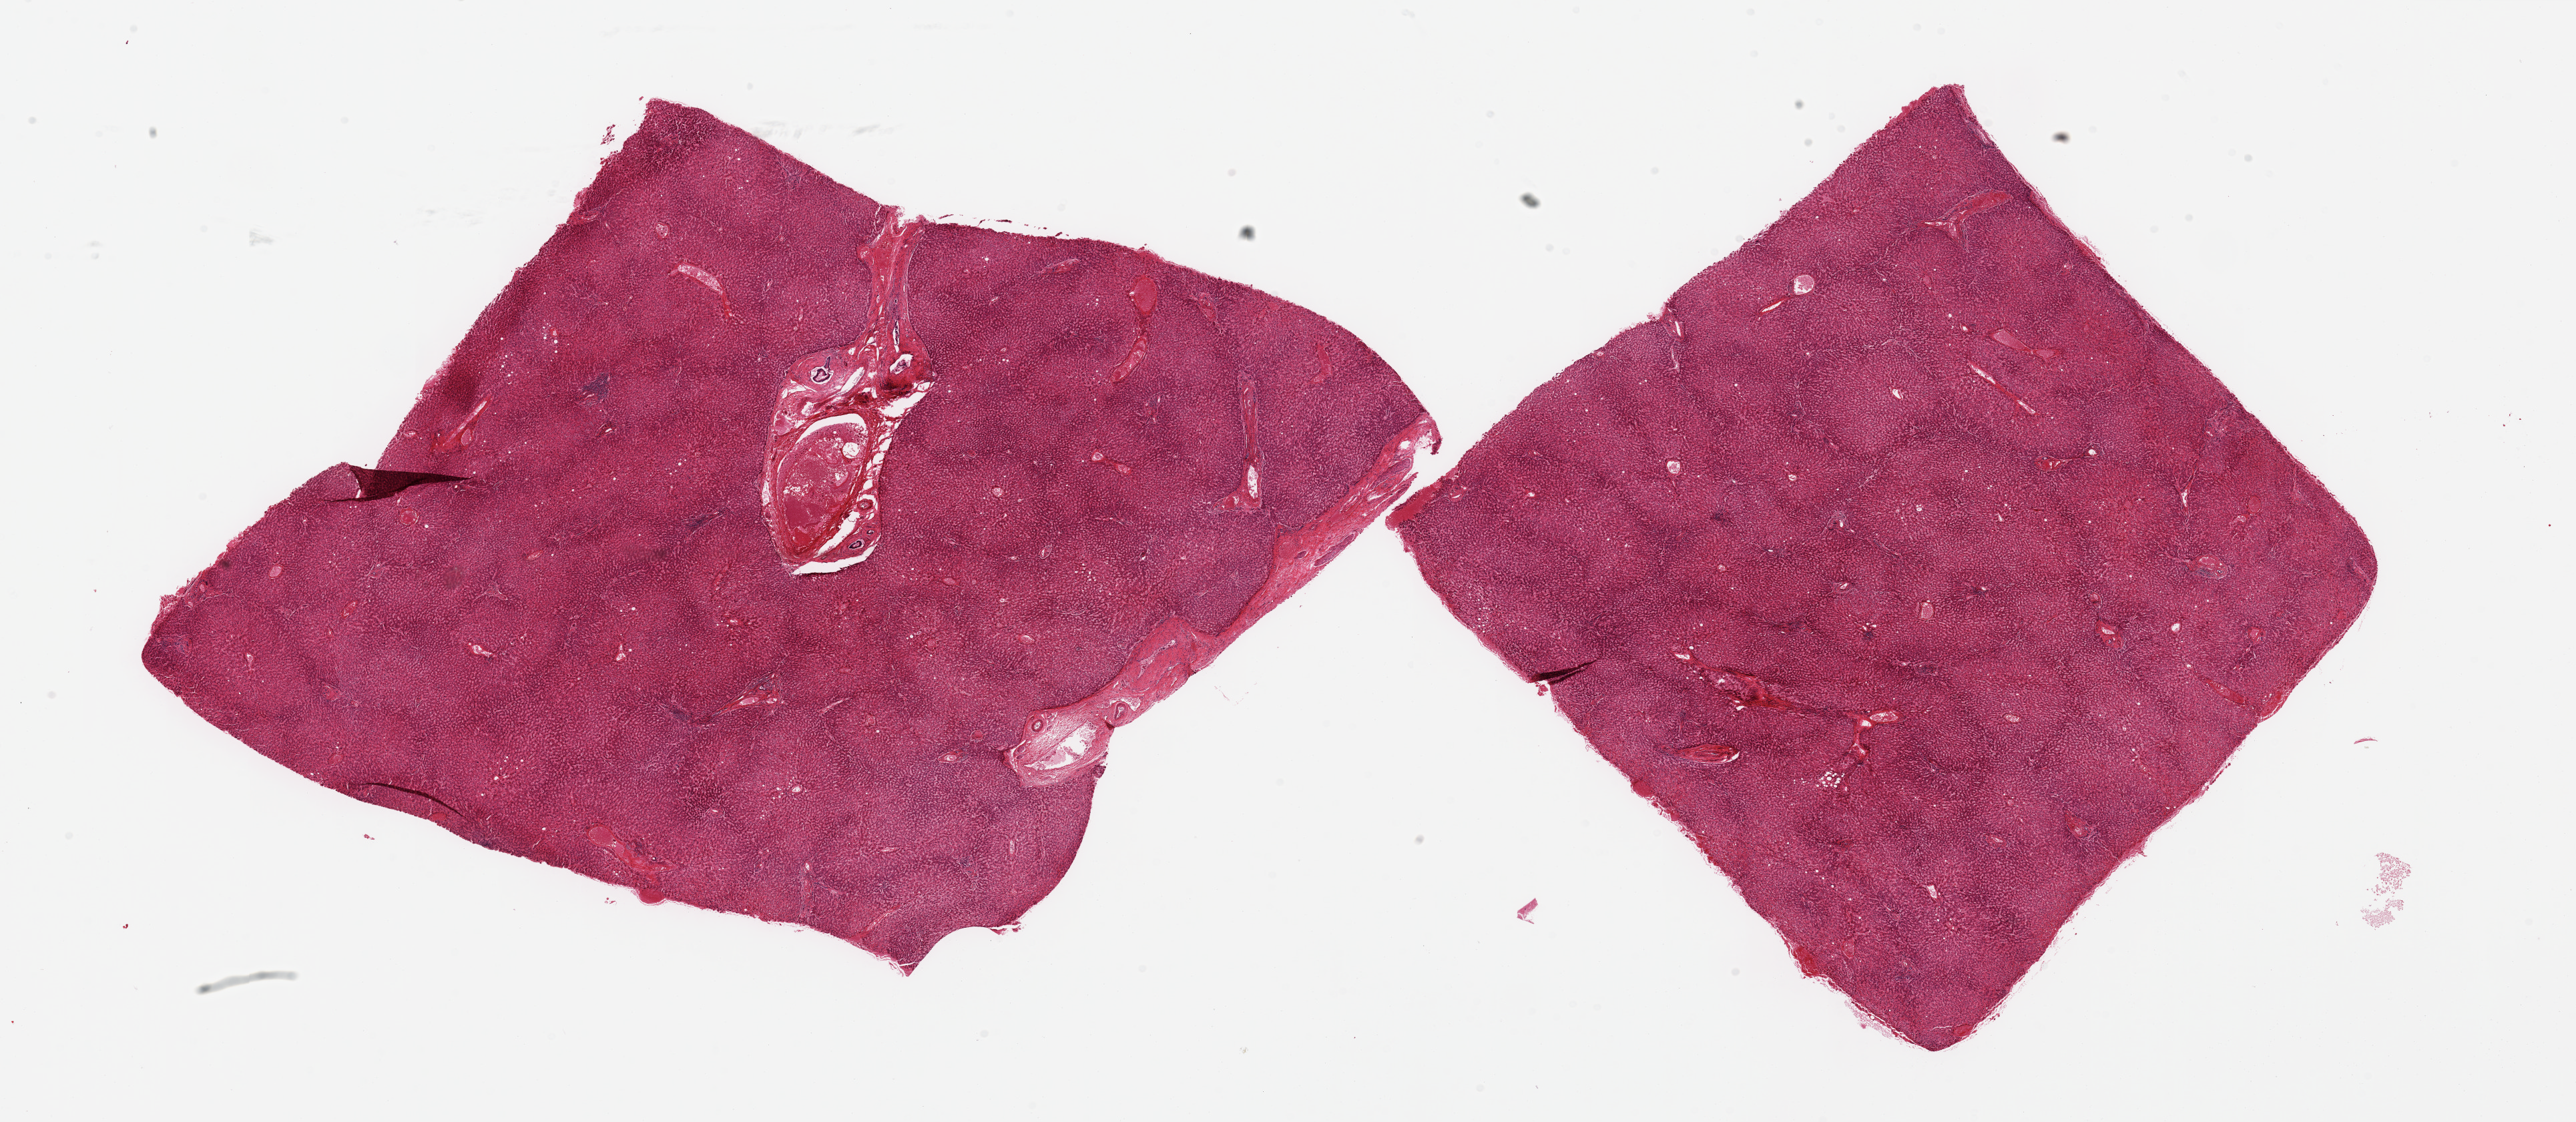
Digitized H&E-stained section, brightfield, whole scanned area (about 30.5 x 13.3 mm, slide scanned at 20x) shown as a low-resolution overview. PAXgene-fixed, paraffin-embedded tissue. Section of liver (target tissue). Tissue donor sample. Donor: male.
Reviewer comment on this tissue sample: 2 pieces; slight degree of congestion.